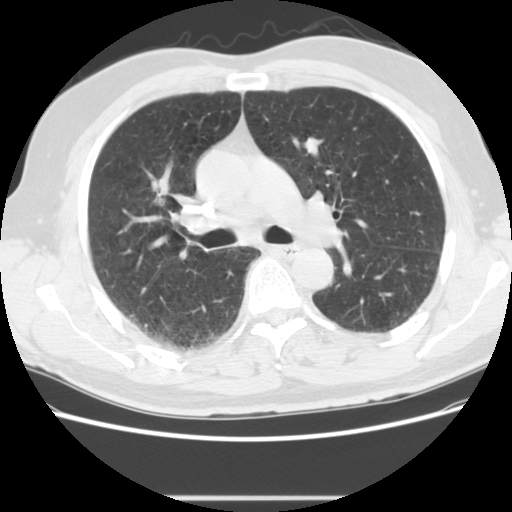
Low-dose screening chest CT, one axial slice; reconstruction kernel STANDARD; lung window (W 1500 / L -600 HU); 512 × 512 image matrix.
Structures marked on this image (expert manual segmentation):
- lesion 1 (tumor, upper lobe of right lung): bounding box [x1, y1, x2, y2] px = [152, 179, 170, 206]